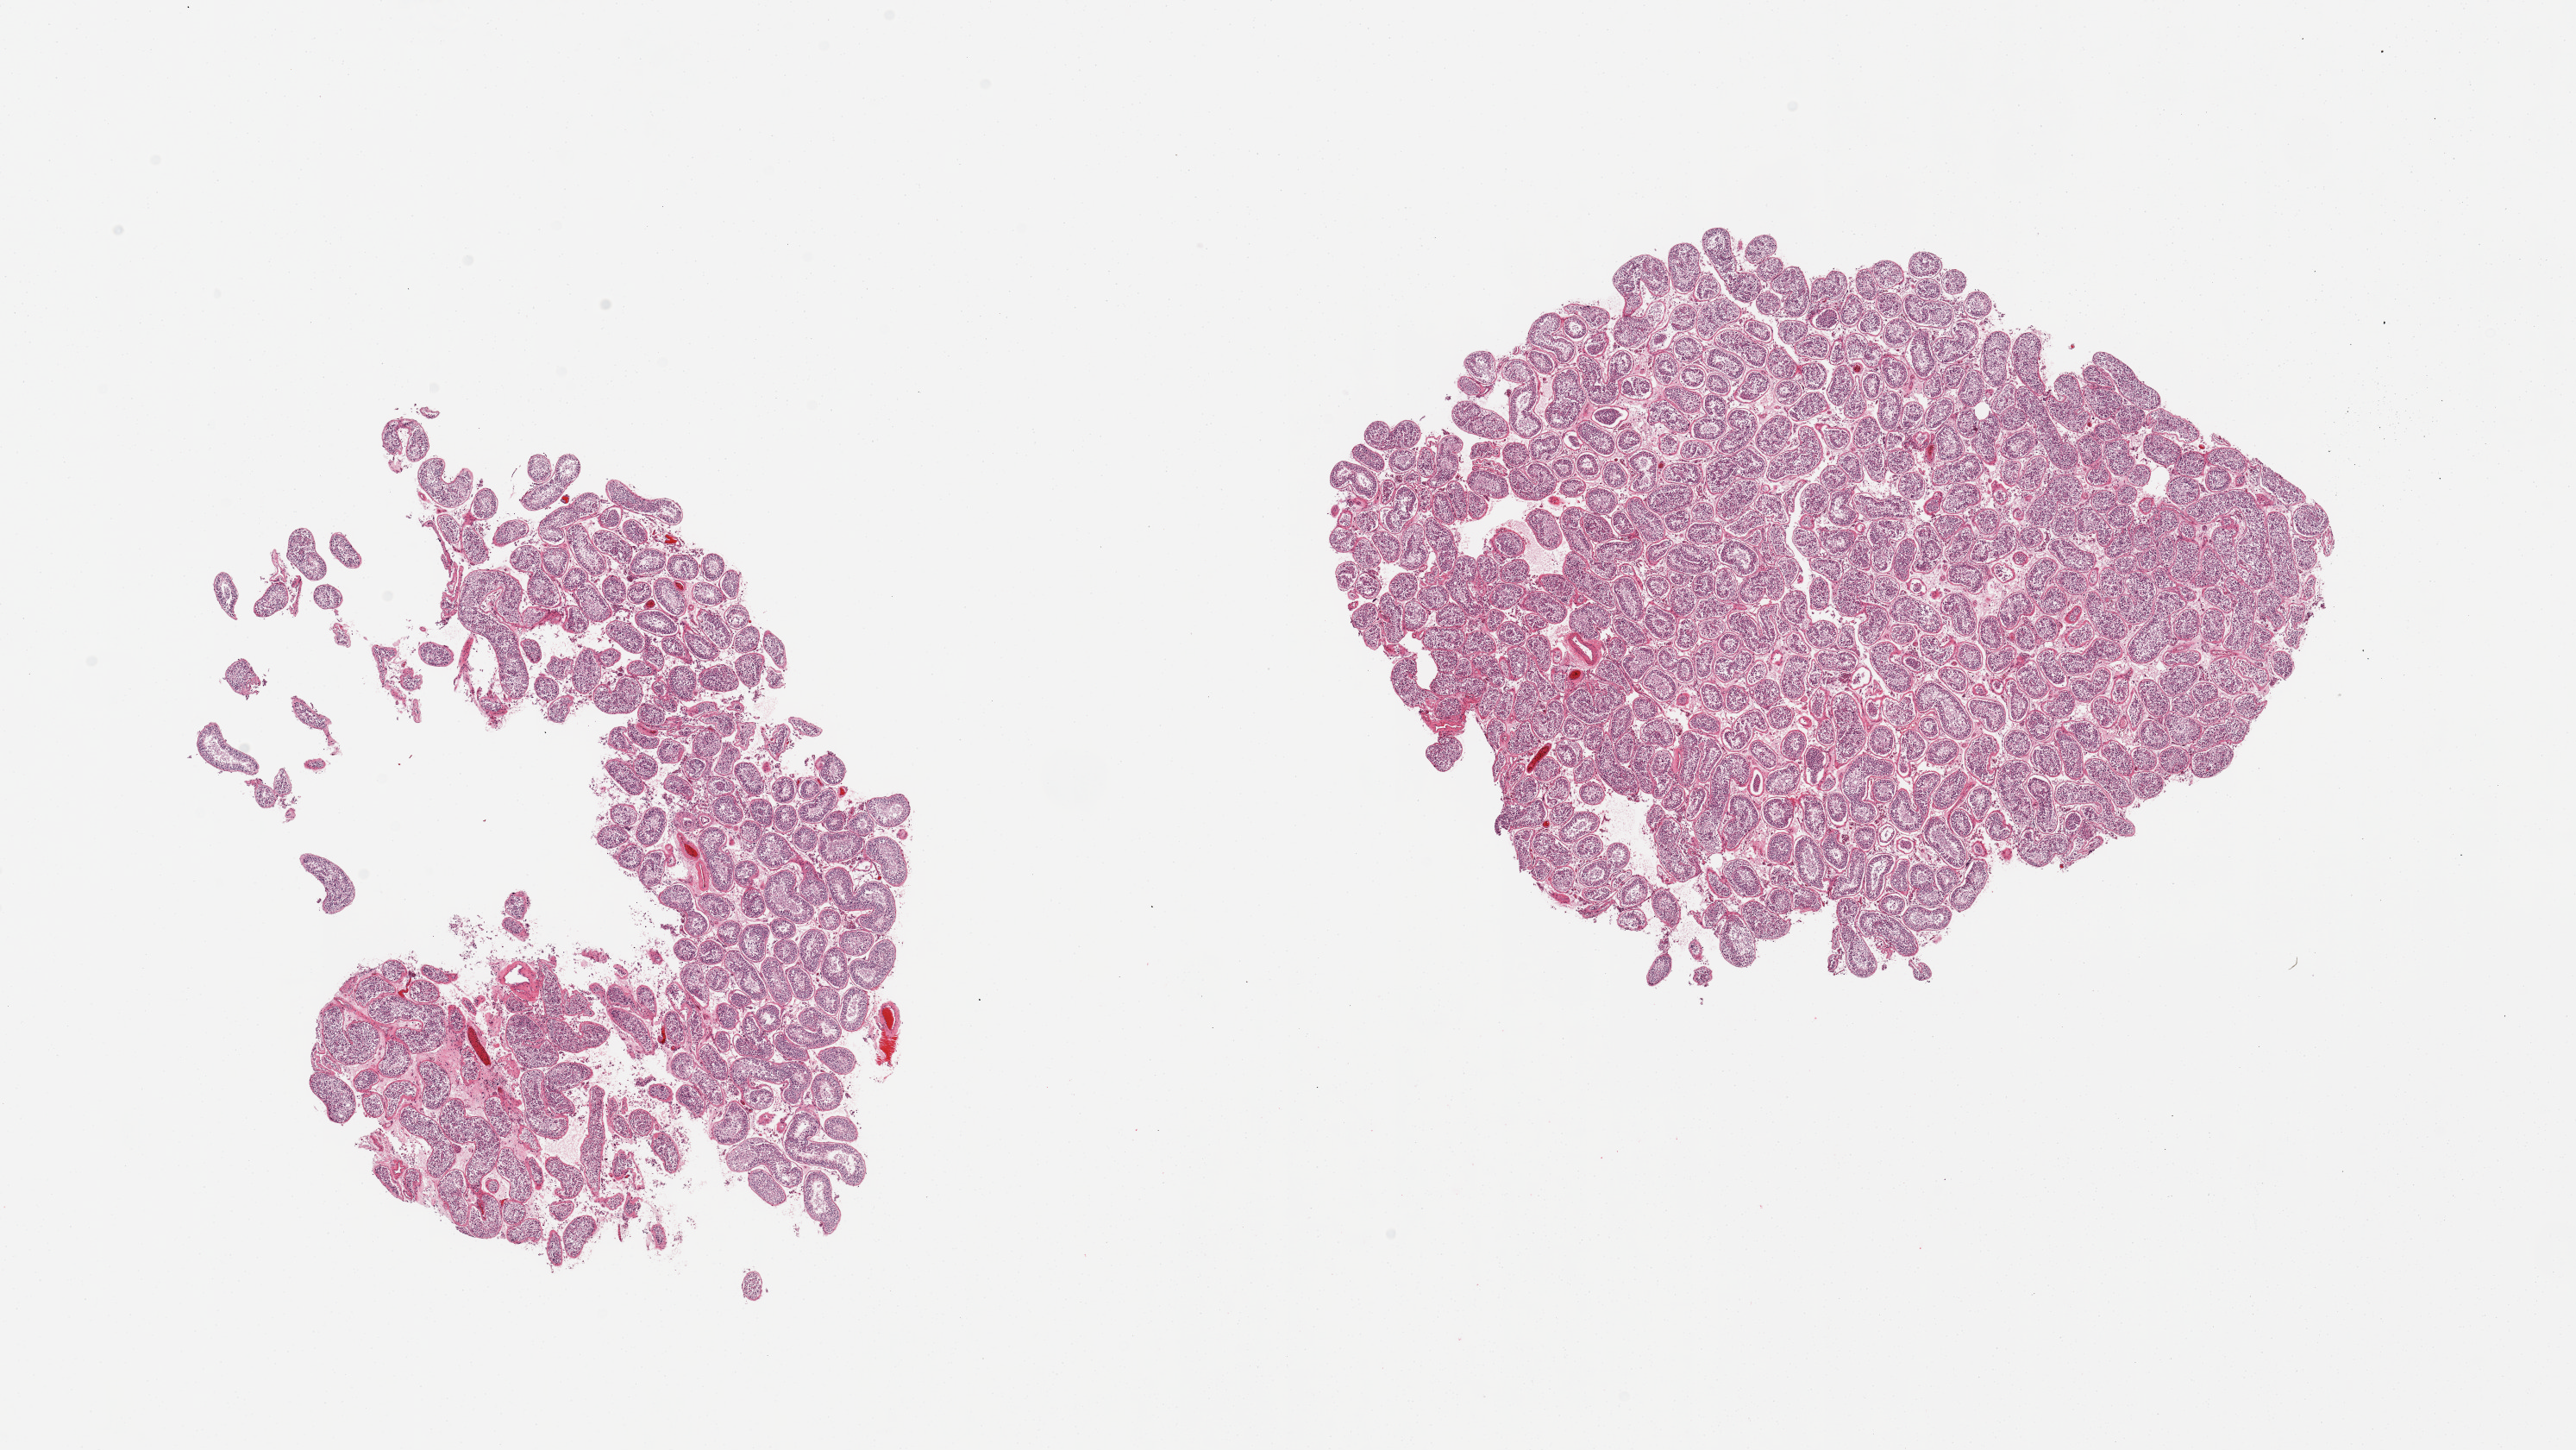
Whole-slide image, haematoxylin and eosin stain — shown as a low-resolution overview of the whole scanned area (about 23.6 x 13.3 mm). PAXgene-fixed paraffin-embedded (PFPE) section. Section of testis (target tissue). Donor tissue sample.
Review note (as recorded): 2 pieces; spermatogenesis.